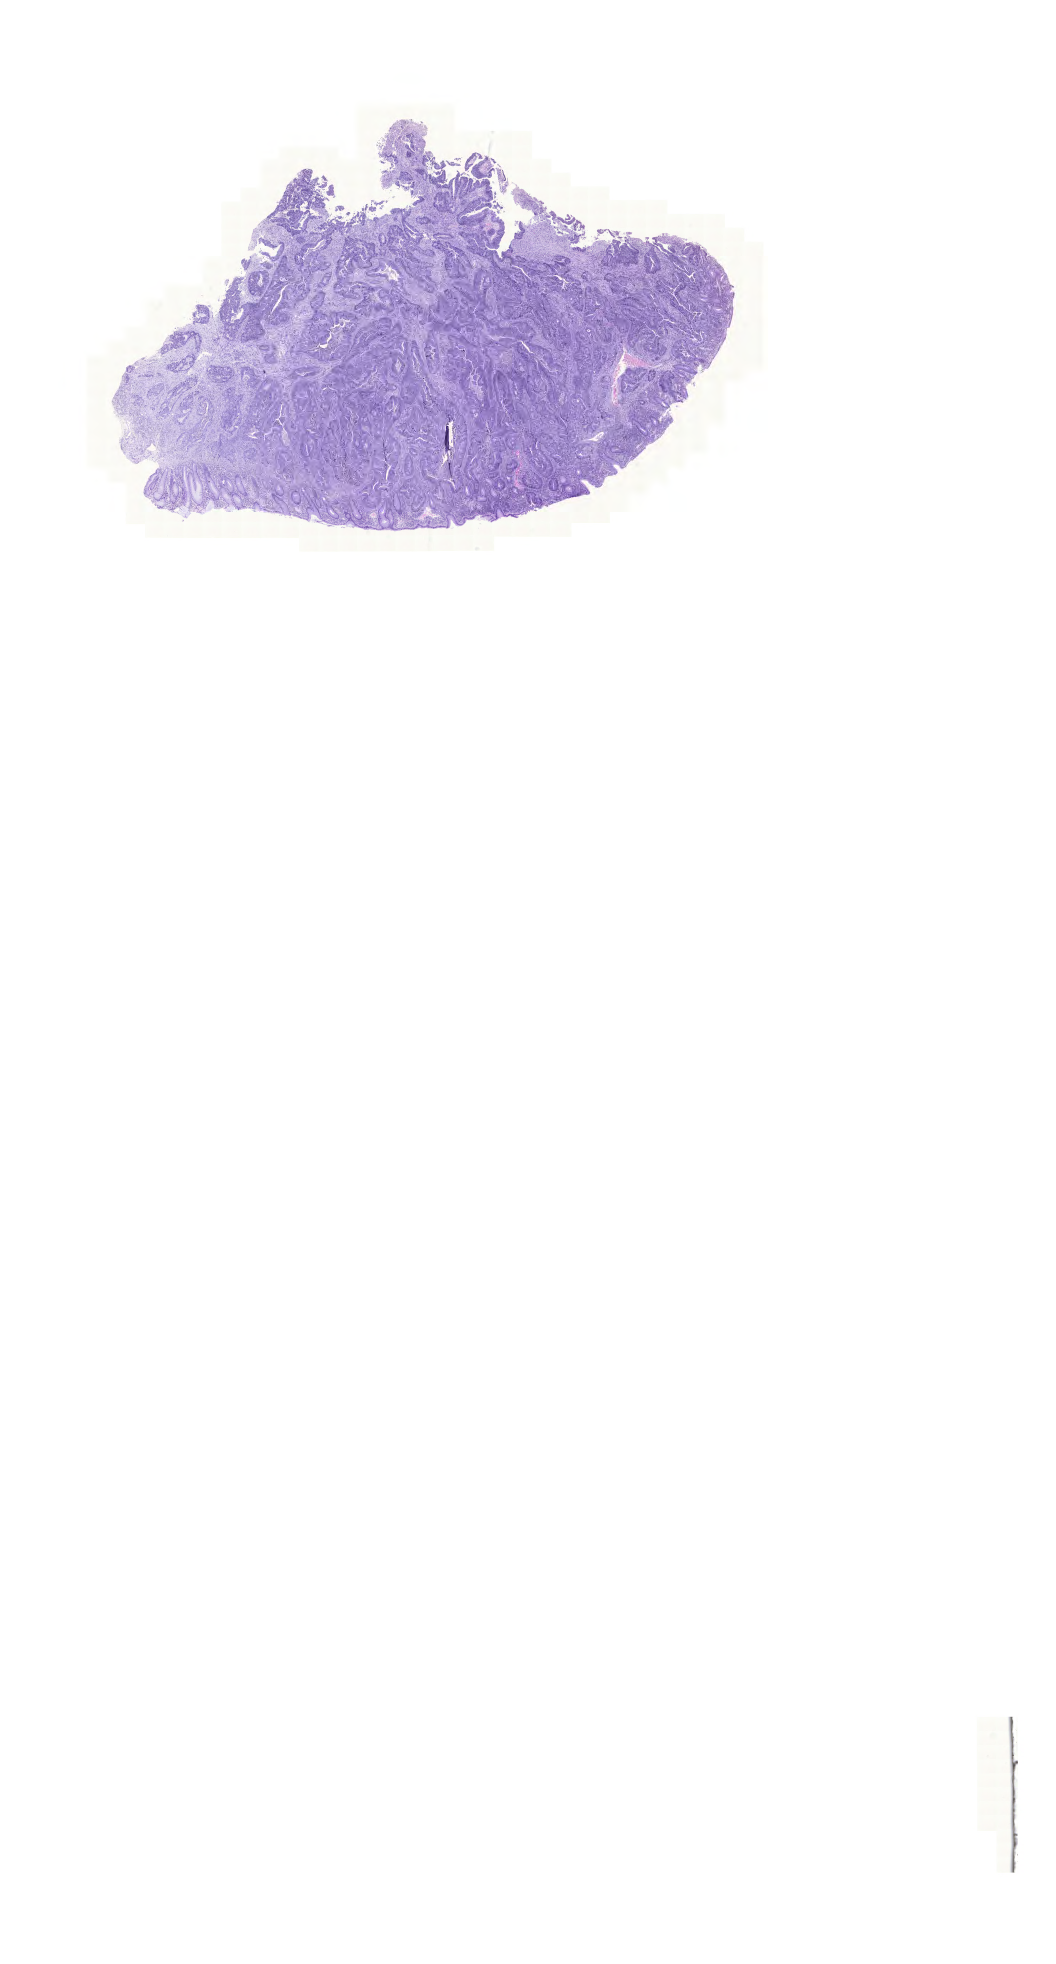
Digitized H&E tissue section (whole slide), shown as a low-resolution overview of the whole scanned area (about 15.7 x 29.2 mm); FFPE section; rectum, primary tumour sample. Patient: male, age at initial diagnosis 75 years.
Histologic diagnosis: Adenocarcinoma, NOS (colon, NOS).